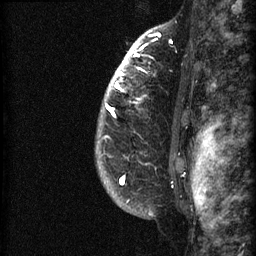
Breast MRI (dynamic contrast-enhanced), one sagittal slice; dynamic contrast-enhanced series, image 2 of 3 at this slice position (ordered by acquisition); 1.5 T; TE 4.2 ms, TR 22.7 ms; 1.5 mm slice thickness; 256 × 256 image matrix, field of view 180 × 180 mm. Female patient, age 48 years. From the clinical record (not read from this slice): setting: breast cancer imaged before/during neoadjuvant chemotherapy; receptor status: triple-negative.
Outlined on this slice (semi-automatically segmented with operator editing):
- analysis volume of interest (the breast-tissue region the enhancement analysis was run in; not a lesion): box from (x=96, y=27) to (x=191, y=180) px
- tumour enhancement mask (voxels above the 90 % enhancement threshold inside the analysis volume of interest): (x=105, y=34)–(x=161, y=180)